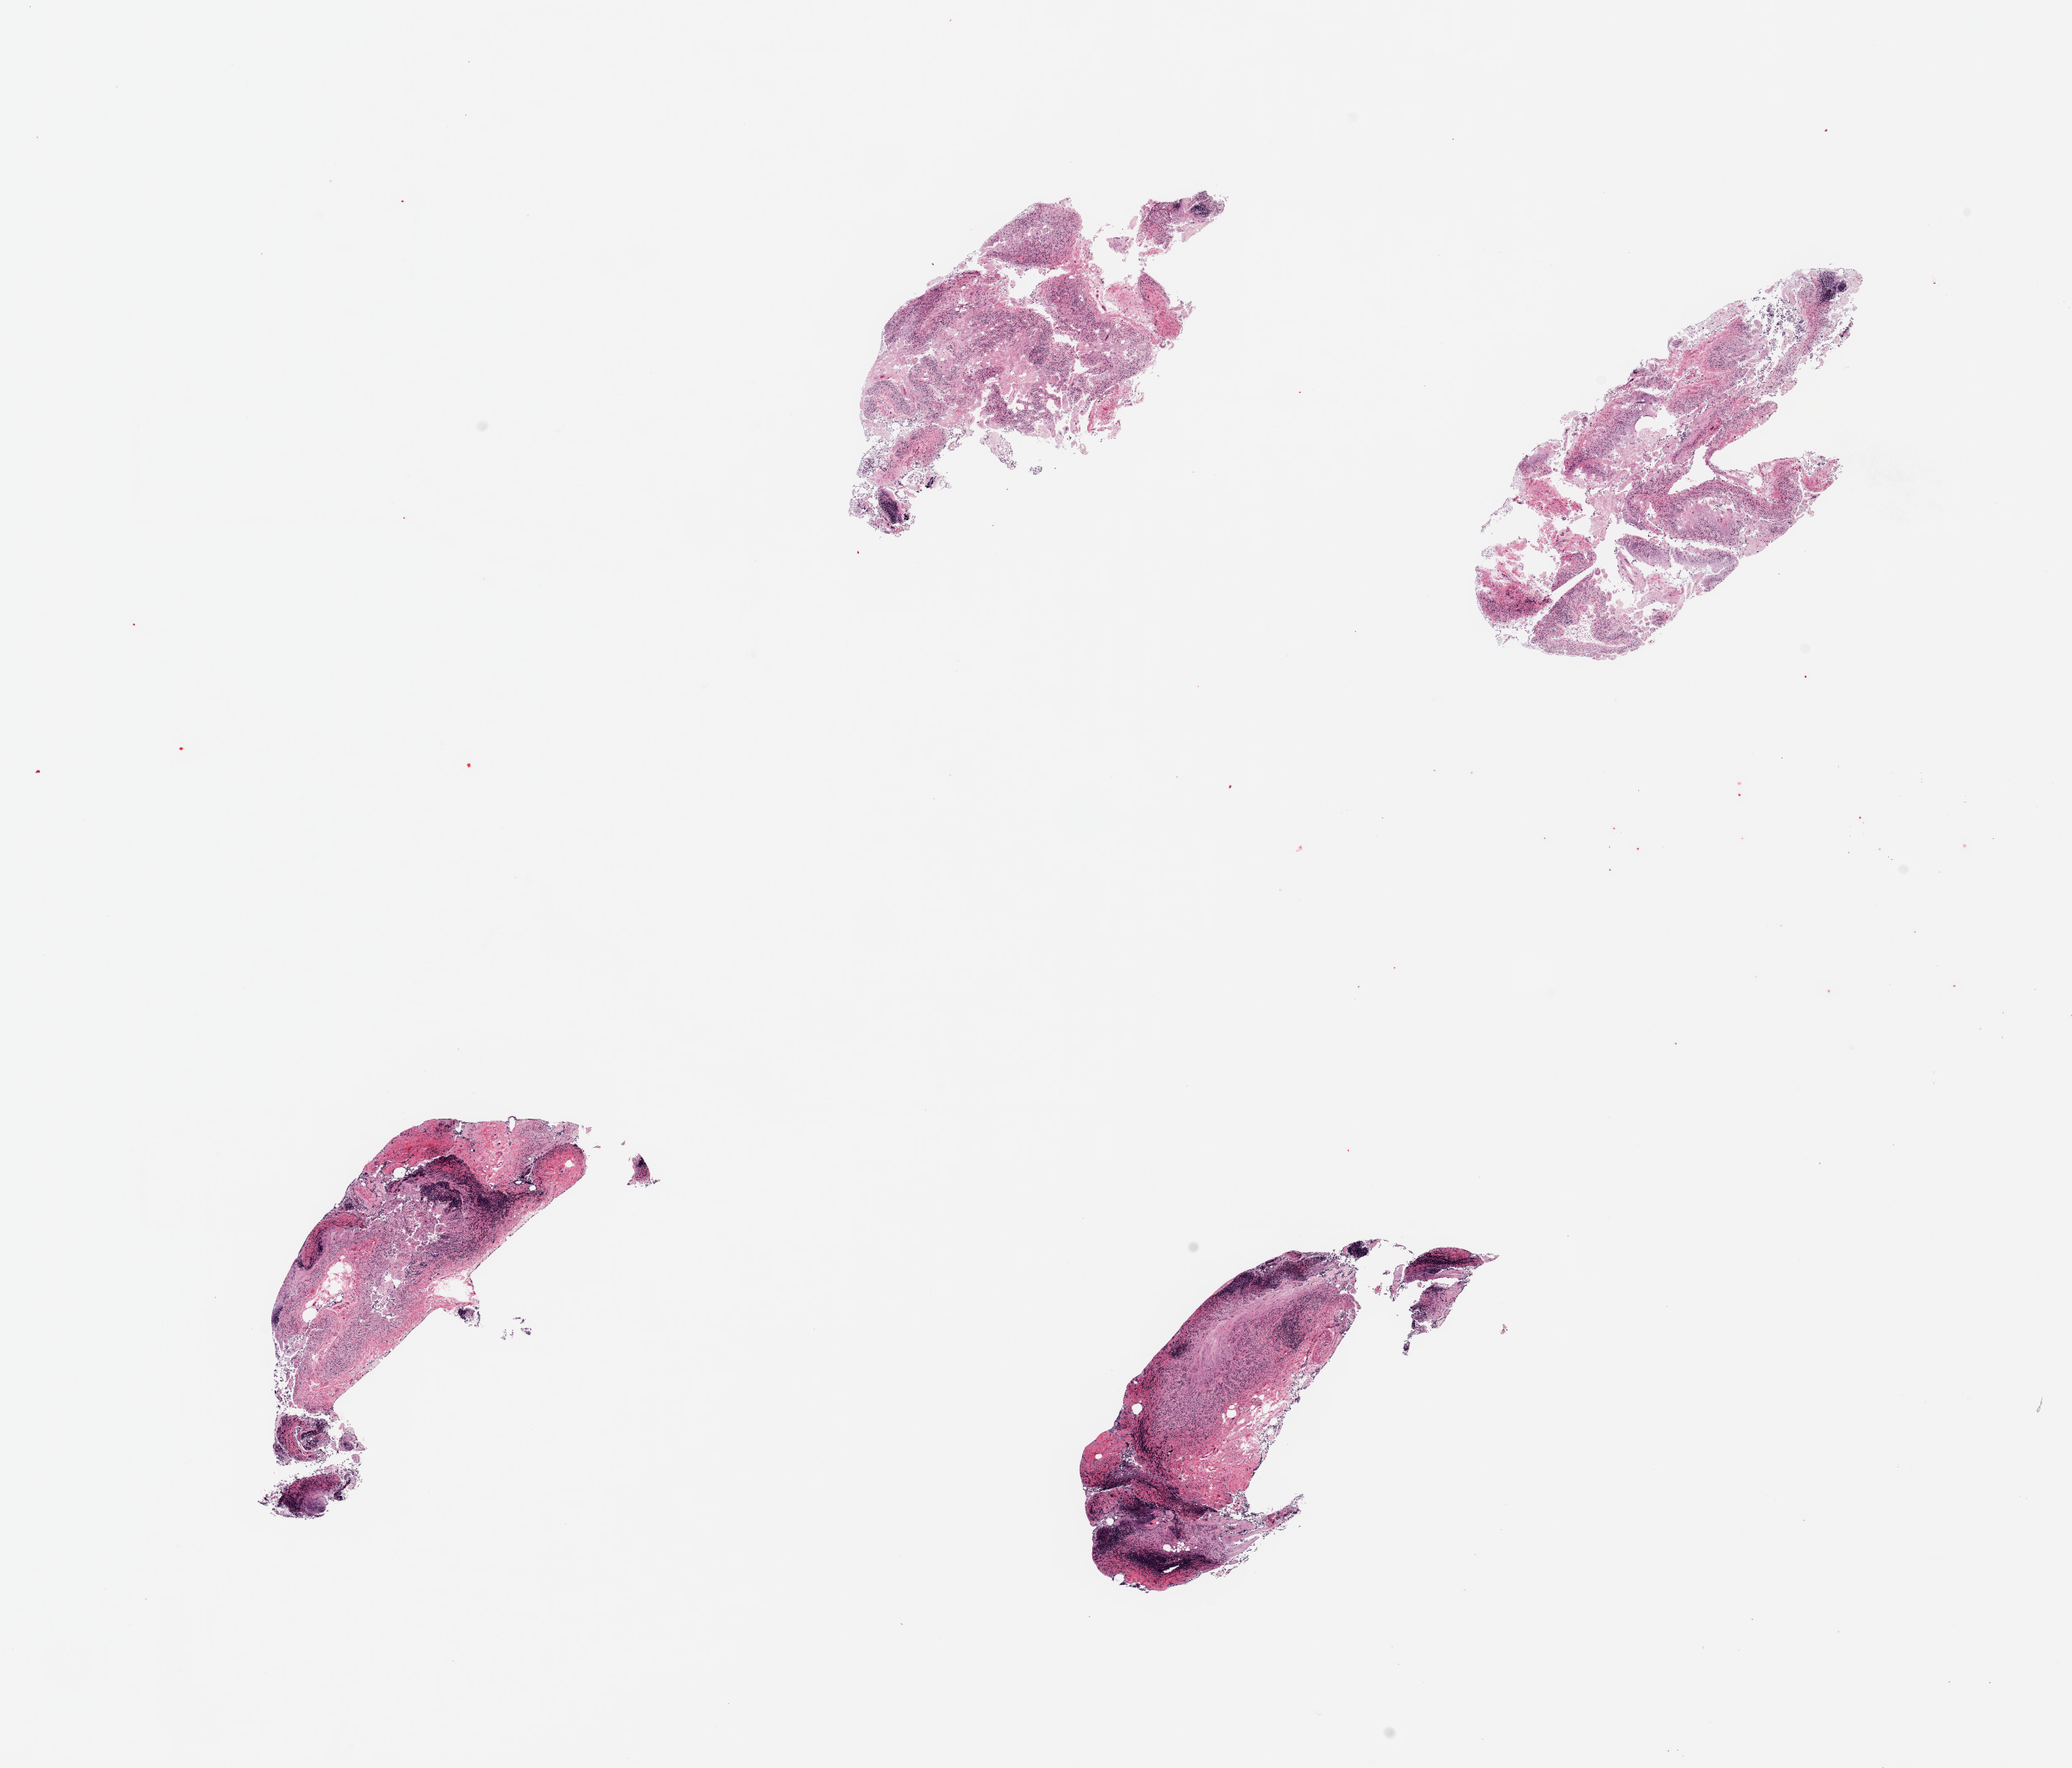
Digitized hematoxylin and eosin (H&E)-stained section, brightfield — a low-resolution overview of the entire scanned area, about 19.7 x 16.8 mm, PAXgene-fixed paraffin-embedded (PFPE) section, section of ileum (target tissue), tissue donor sample.
Review note (as recorded): 4 pieces; lymphoid tissue present but too autolyzed for study.